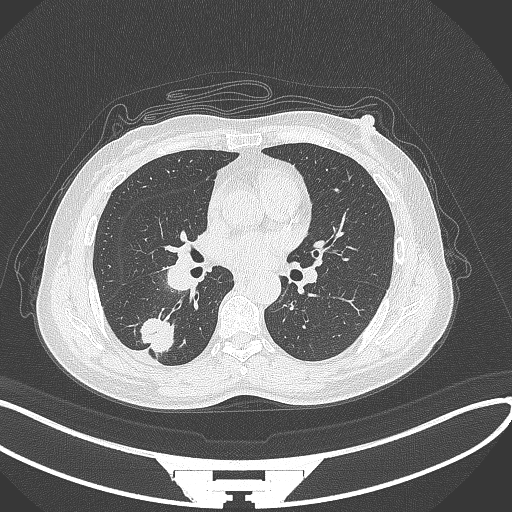
Chest CT, one axial slice. Slice 152 of 352 in the series (ordered by position). 120 kVp. Lung window (W 1500 / L -600 HU). 1 mm slice thickness. 512 × 512 image matrix, field of view 400 × 400 mm. Patient: female, 55 years. Case-level facts recorded for this patient, not image findings: clinical TNM (as recorded): T1c N1 M0.
Annotated regions visible in this slice (bounding box drawn by a radiologist):
- lung tumour (recorded histology: adenocarcinoma): bounding box <133,311,179,357> (left, top, right, bottom; pixels)